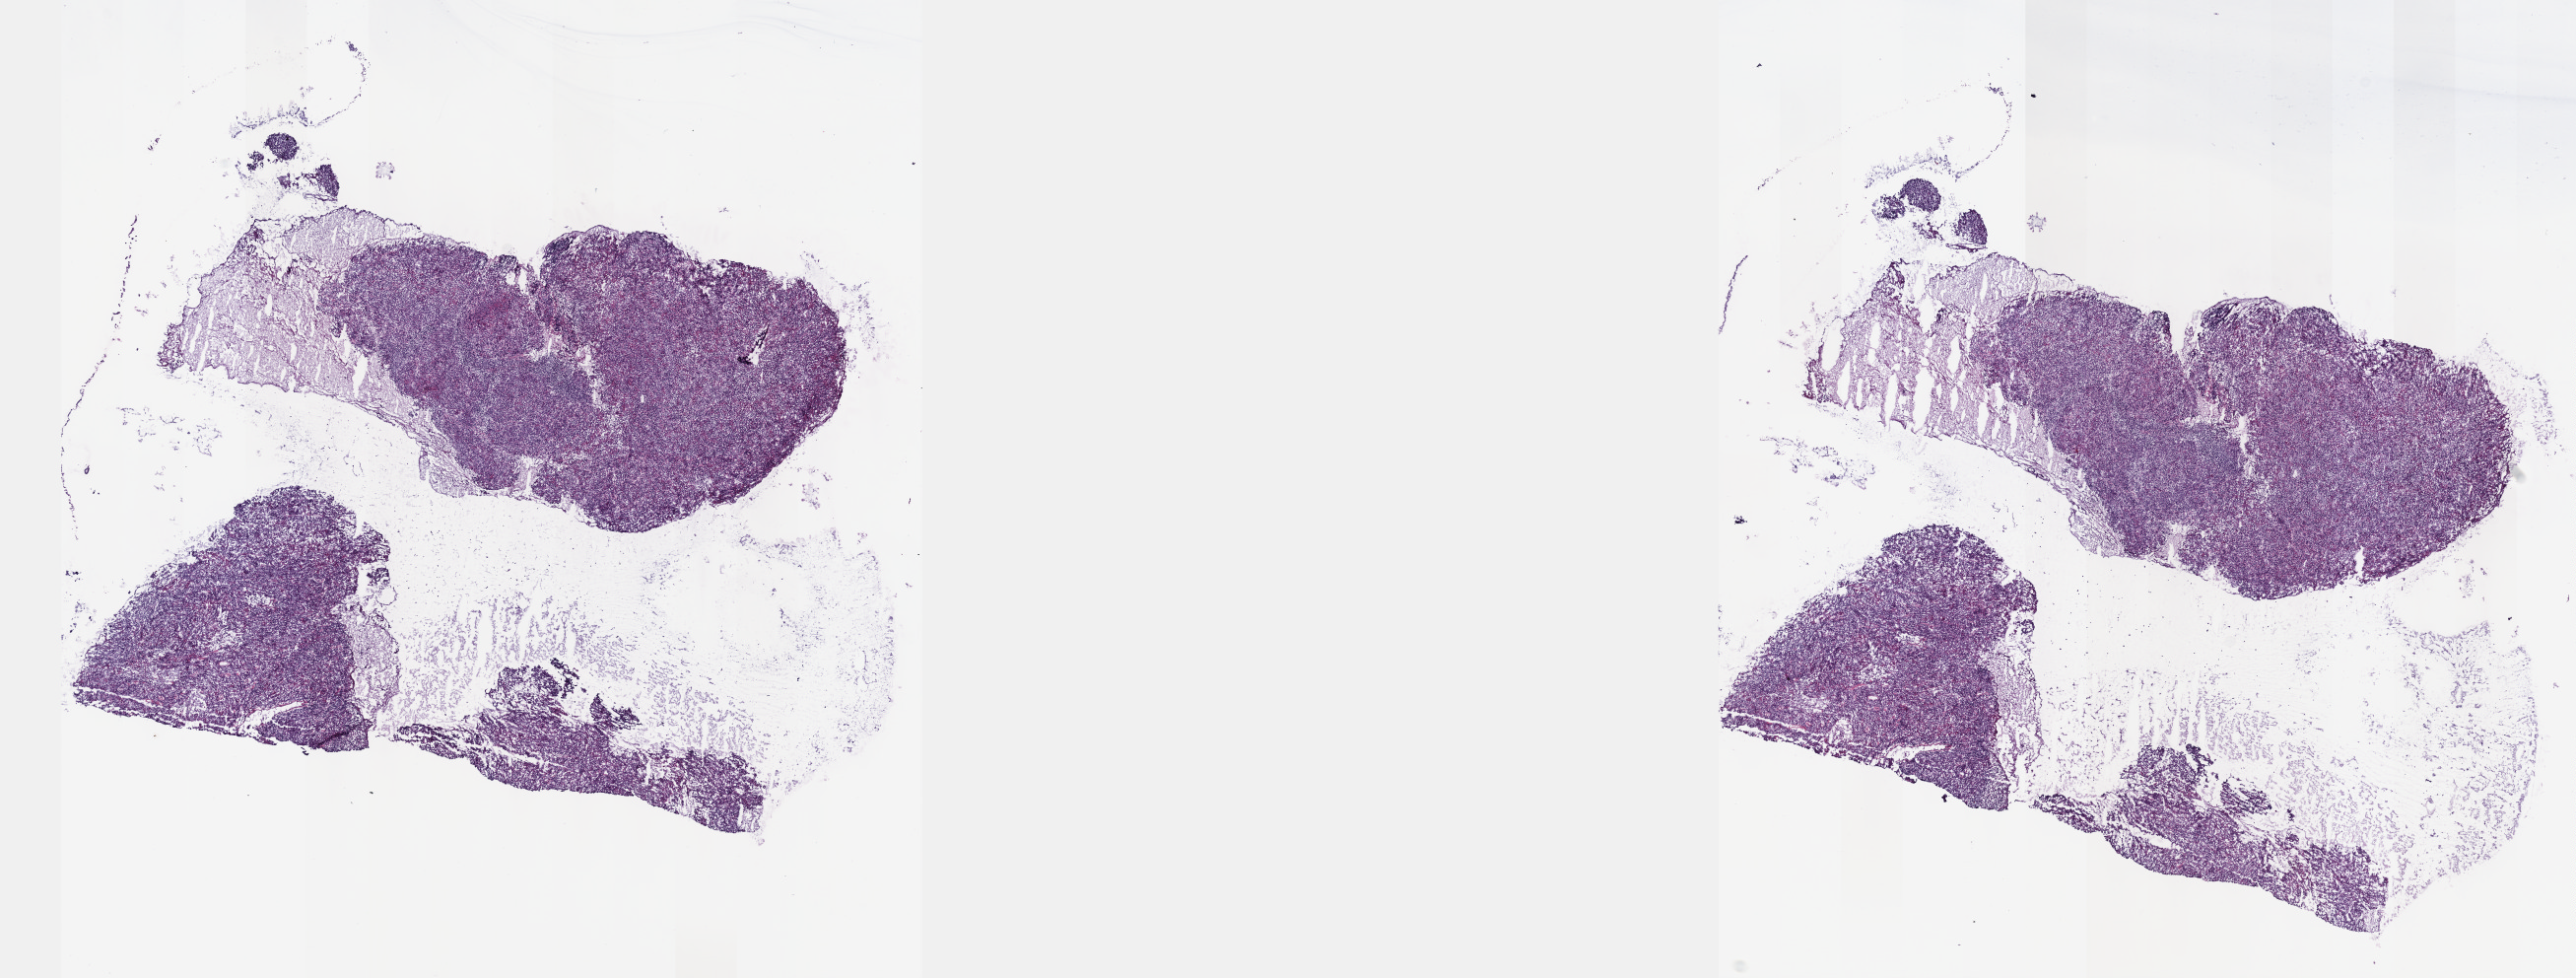
Hematoxylin and eosin (H&E) stained whole-slide image — shown as a low-resolution overview of the whole scanned area (about 21.1 x 8.0 mm), frozen section, sample: primary tumour, cervix. Female, age 75 years at initial diagnosis. Histologic grade: G3 (poorly differentiated). Composition of this section per pathologist review: tumour cells 75%, tumour nuclei 75%, normal cells 5%, stromal cells 2%, necrosis 18%. Inflammatory infiltration, as recorded: lymphocyte infiltration 3%, monocyte infiltration 0%, neutrophil infiltration 2%.
Histologic diagnosis: Squamous cell carcinoma, NOS (cervix uteri). FIGO stage: IIB.